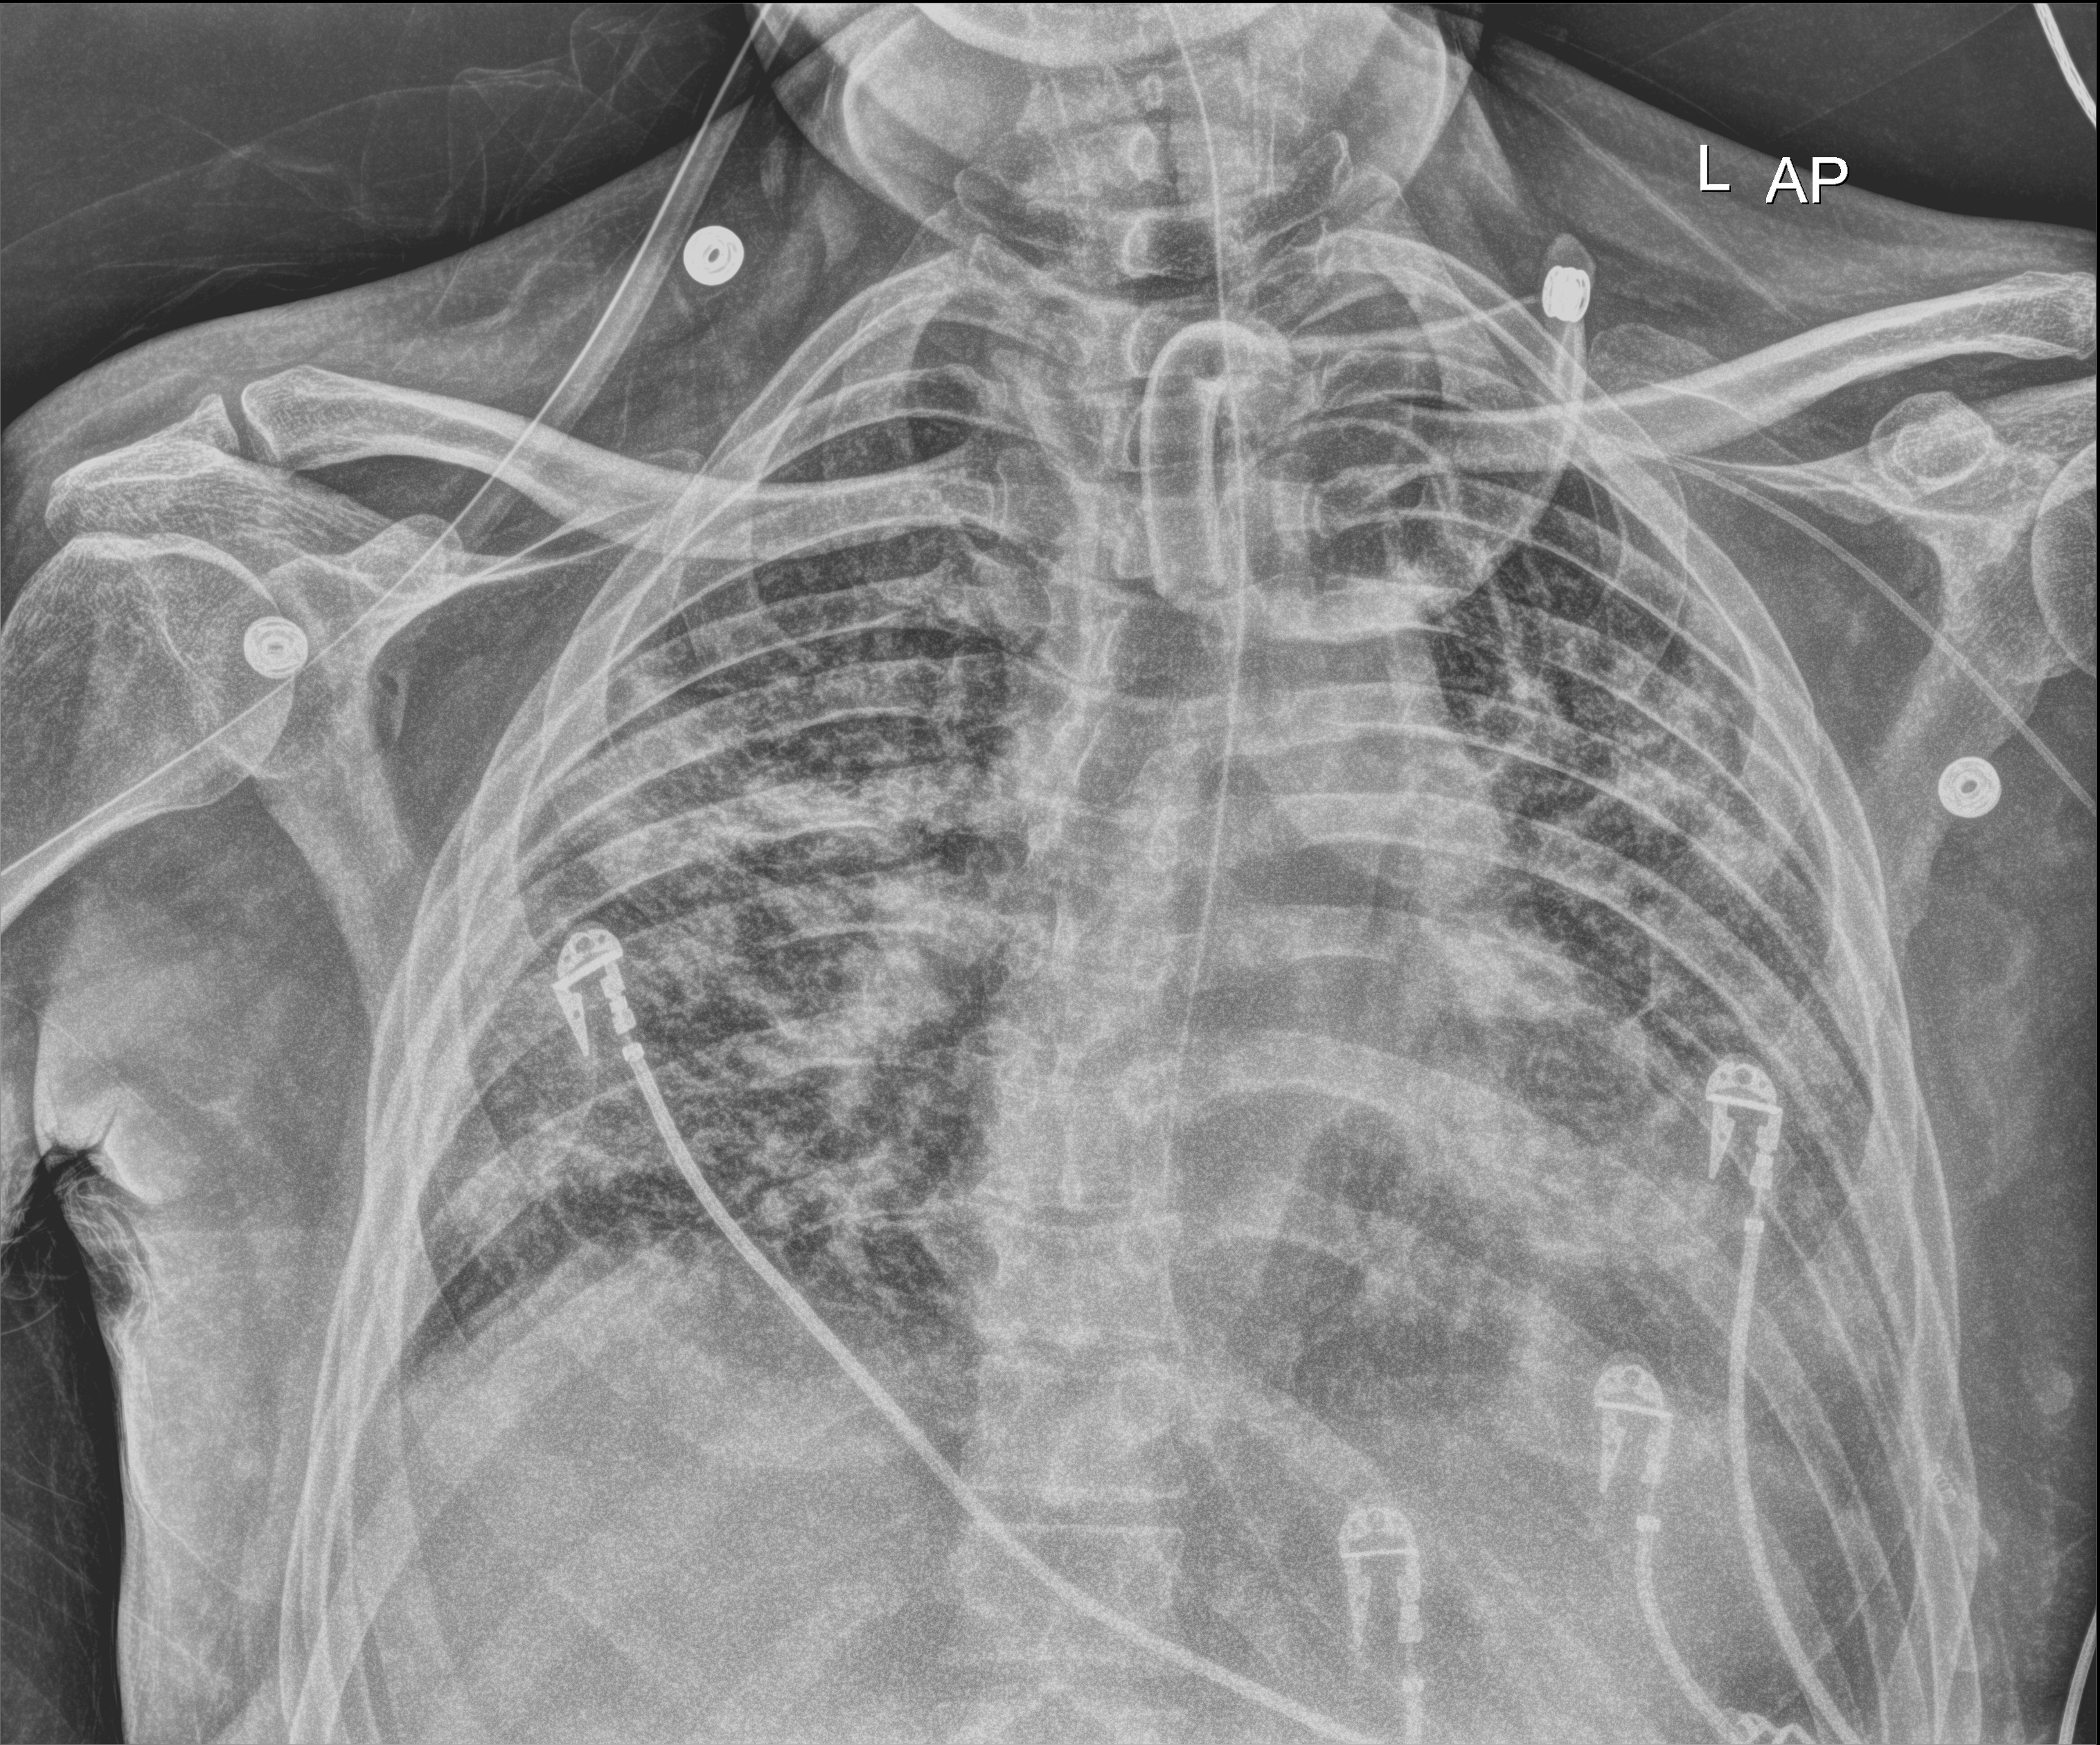
Chest X-ray. Male patient hospitalised with COVID-19, age 18–59 years.
Admission-level facts for this patient (not findings on this image; timing relative to this image not recorded):
- mechanically ventilated during this hospital stay: yes
- admitted to intensive care during this hospital stay: yes
- diabetes (admission record): no